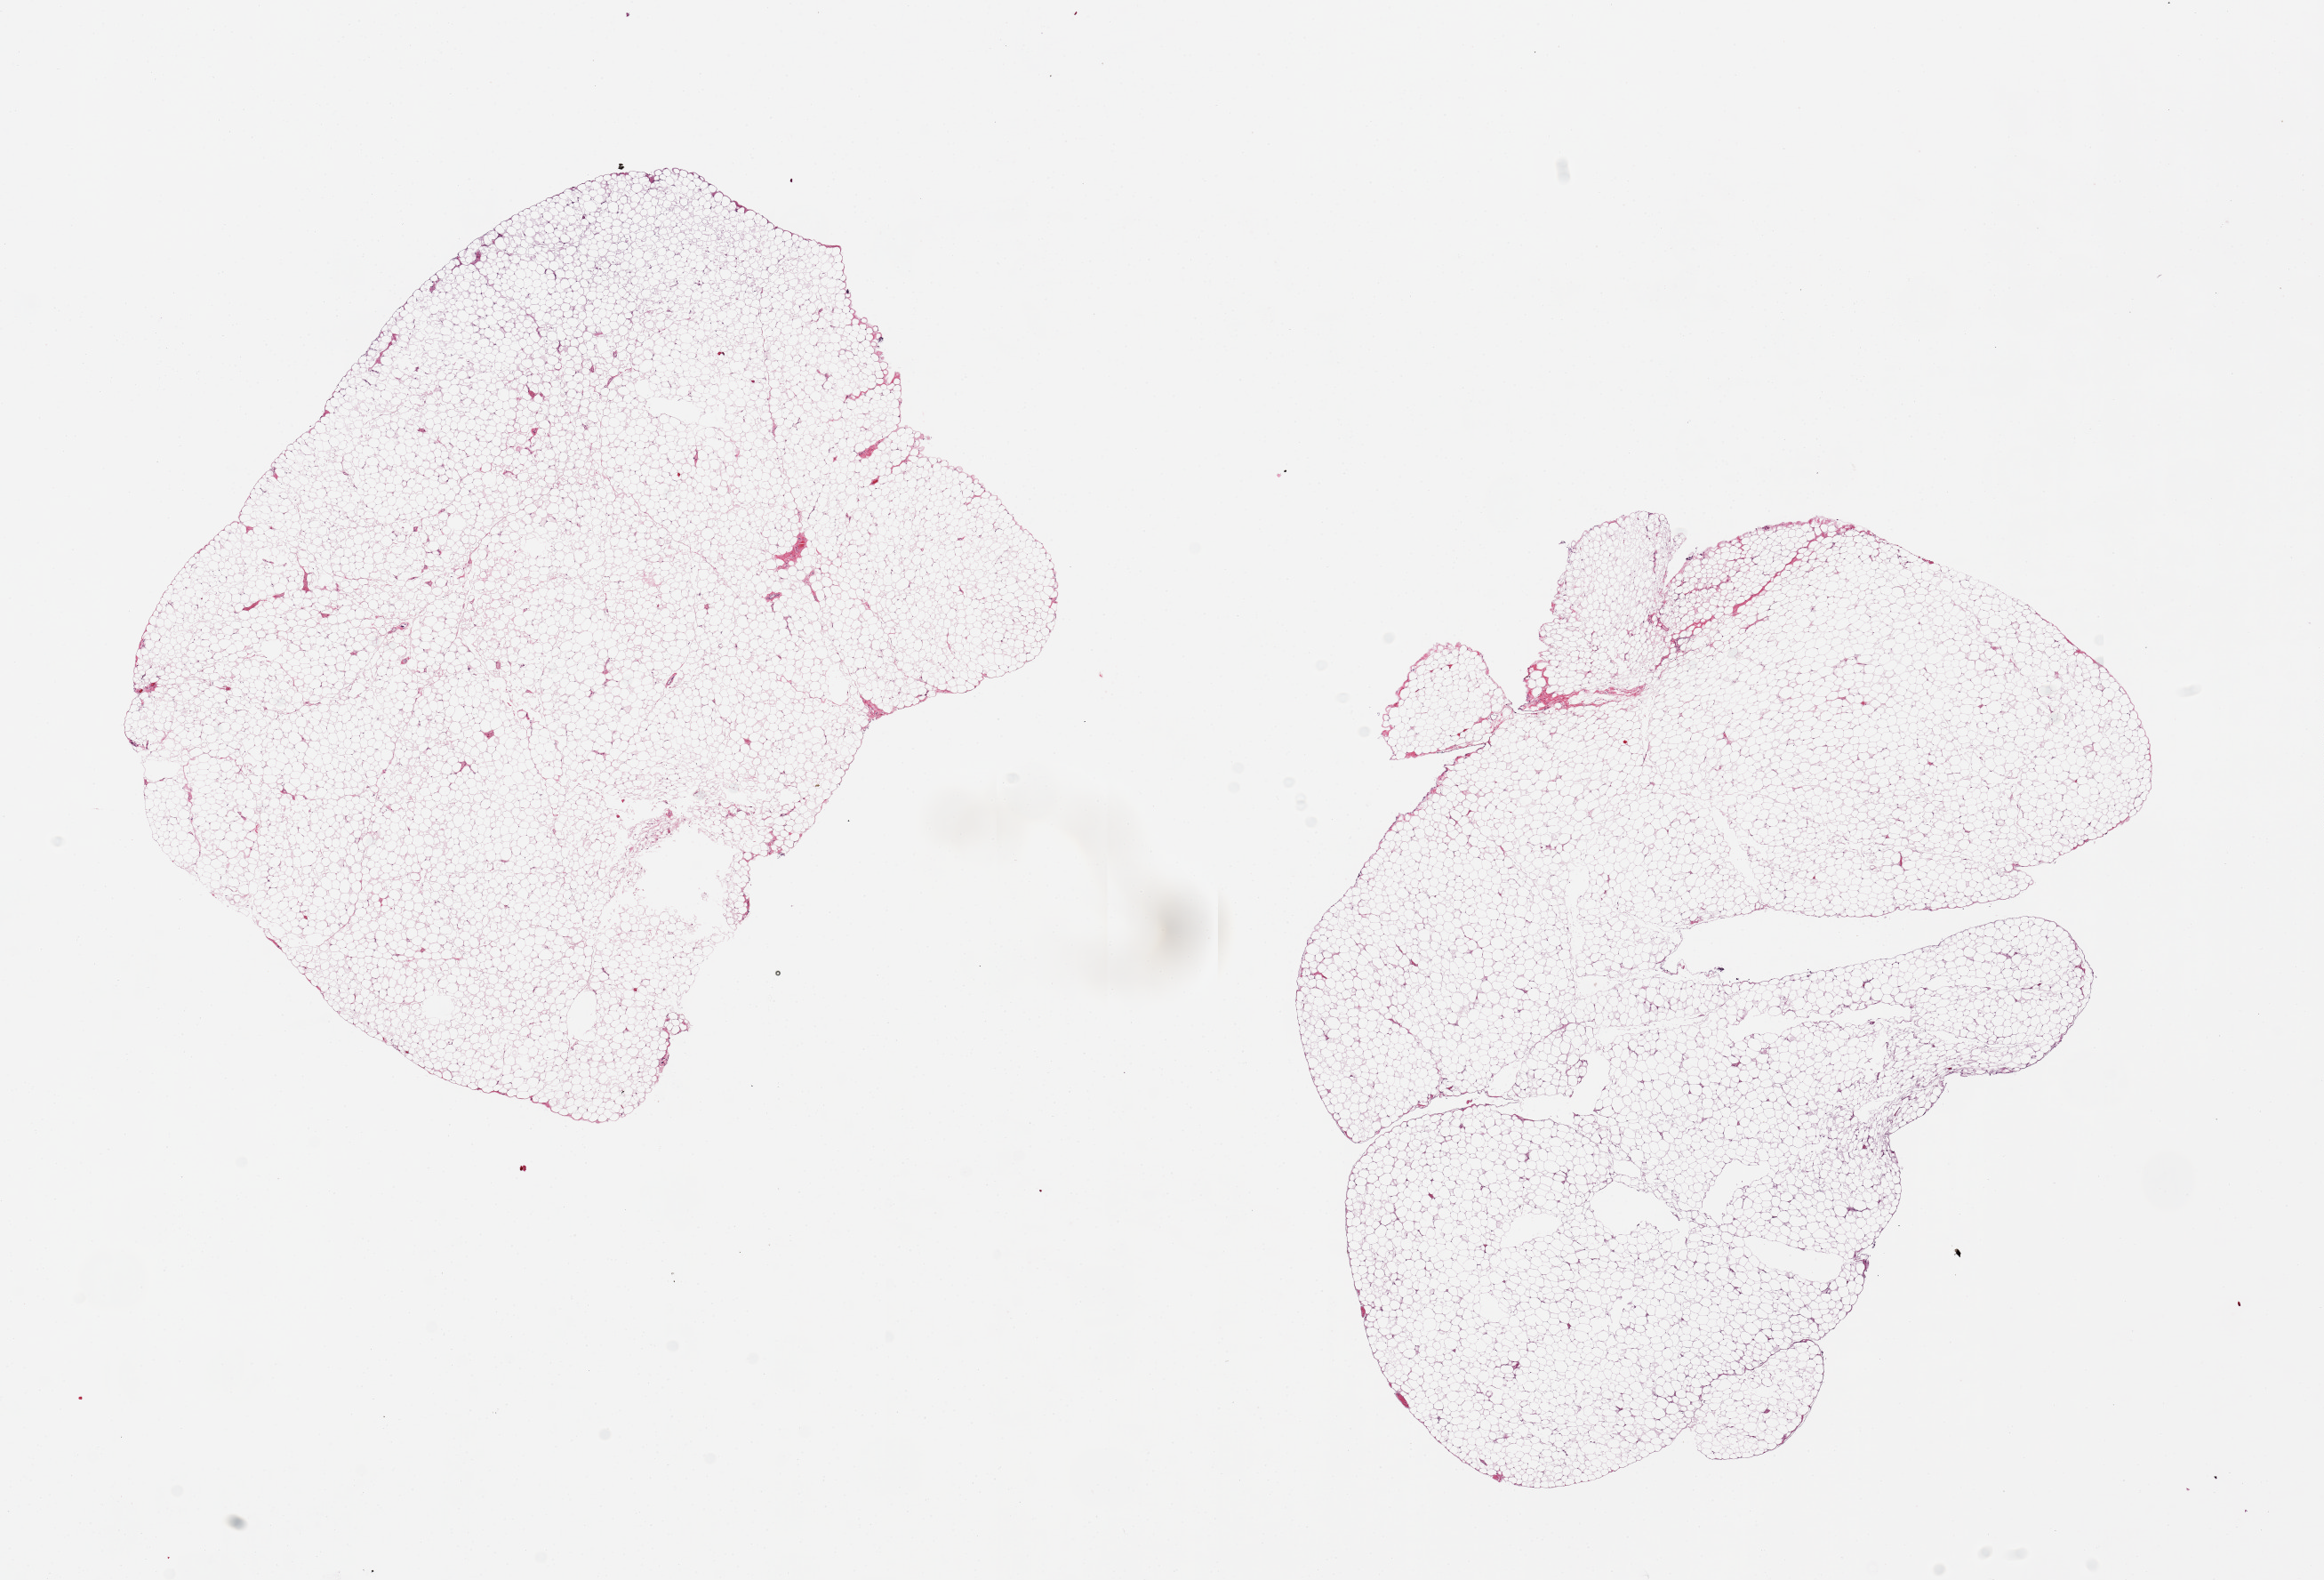
Whole-slide image, hematoxylin and eosin (H&E) stain — whole scanned area (about 20.7 x 14.1 mm) shown as a low-resolution overview, PAXgene-fixed, paraffin-embedded tissue, target tissue: omentum, donor tissue sample. Donor: female.
Reviewer comment on this tissue sample: 2 pieces. 8x6.5 & 9x7.5mm; well fixed.